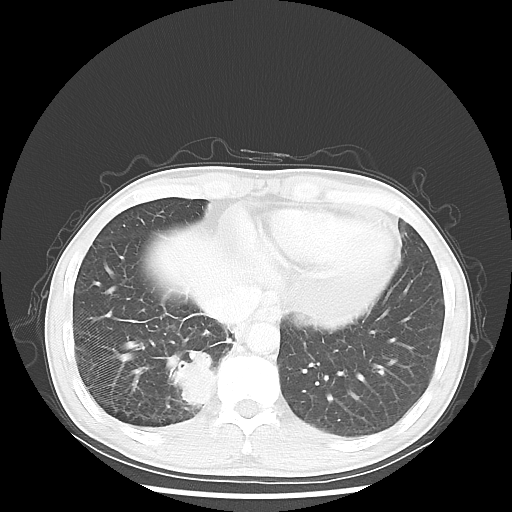
Chest CT, one axial slice. Slice 12 of 58 in the series (ordered by position). Reconstruction kernel LUNG. 100 kVp. Lung window (W 1500 / L -600 HU). 5 mm slice thickness. 512 × 512 image matrix, field of view 360 × 360 mm. Patient: male, 56 years. From the clinical record (not read from this slice): clinical TNM (as recorded): T2 N1 M1; histopathological grade: G1.
Annotated regions visible in this slice (bounding box drawn by a radiologist):
- lung tumour (recorded histology: adenocarcinoma): bounding box <160,343,219,406> (left, top, right, bottom; pixels)